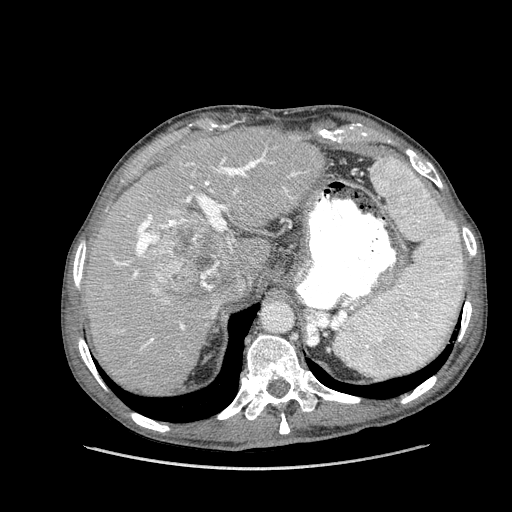
Contrast-enhanced abdominal CT (liver protocol), one axial slice. Slice 107 of 162 in the series (ordered by position). Reconstruction kernel STANDARD. Soft-tissue window (W 400 / L 40 HU). 2.5 mm slice thickness. 512 × 512 image matrix, field of view 400 × 400 mm. Case-level facts recorded for this patient, not image findings: diagnosis: hepatocellular carcinoma (patient treated with transarterial chemoembolisation; whether this scan precedes or follows treatment is not stated here); TNM stage (as recorded): Stage-IIIA; Child-Pugh class: A; tumour nodularity: multinodular; tumour size: 9.9 cm.
Annotated regions visible in this slice (semi-automatic segmentation, software-assisted and operator-edited):
- liver parenchyma outside the tumour (the mass and vessels are separate outlines, so this box may not span the whole liver): bounding box <84,126,324,394> (left, top, right, bottom; pixels)
- mass: <153,214,233,300>
- liver vessels: <114,152,298,350>